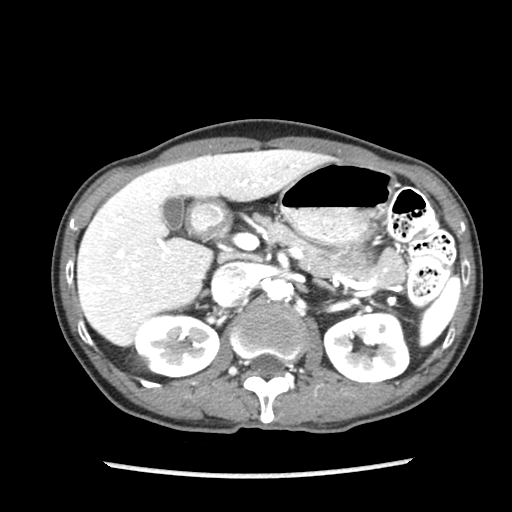
Contrast-enhanced abdominal CT (liver protocol), one axial slice; position 49 of 87 along the scan axis; reconstruction kernel STANDARD; 140 kVp; soft-tissue window (W 400 / L 40 HU); 2.5 mm slice thickness; 512 × 512 image matrix, field of view 300 × 300 mm. From the clinical record (not read from this slice): diagnosis: hepatocellular carcinoma (patient treated with transarterial chemoembolisation; whether this scan precedes or follows treatment is not stated here); TNM stage (as recorded): Stage-IIIB; Child-Pugh class: A; tumour differentiation: well differentiated; tumour nodularity: uninodular.
Structures marked on this image (semi-automatic segmentation, software-assisted and operator-edited):
- liver parenchyma outside the tumour (the mass and vessels are separate outlines, so this box may not span the whole liver): box from (x=78, y=148) to (x=330, y=346) px
- liver vessels: (x=85, y=165)–(x=295, y=293)